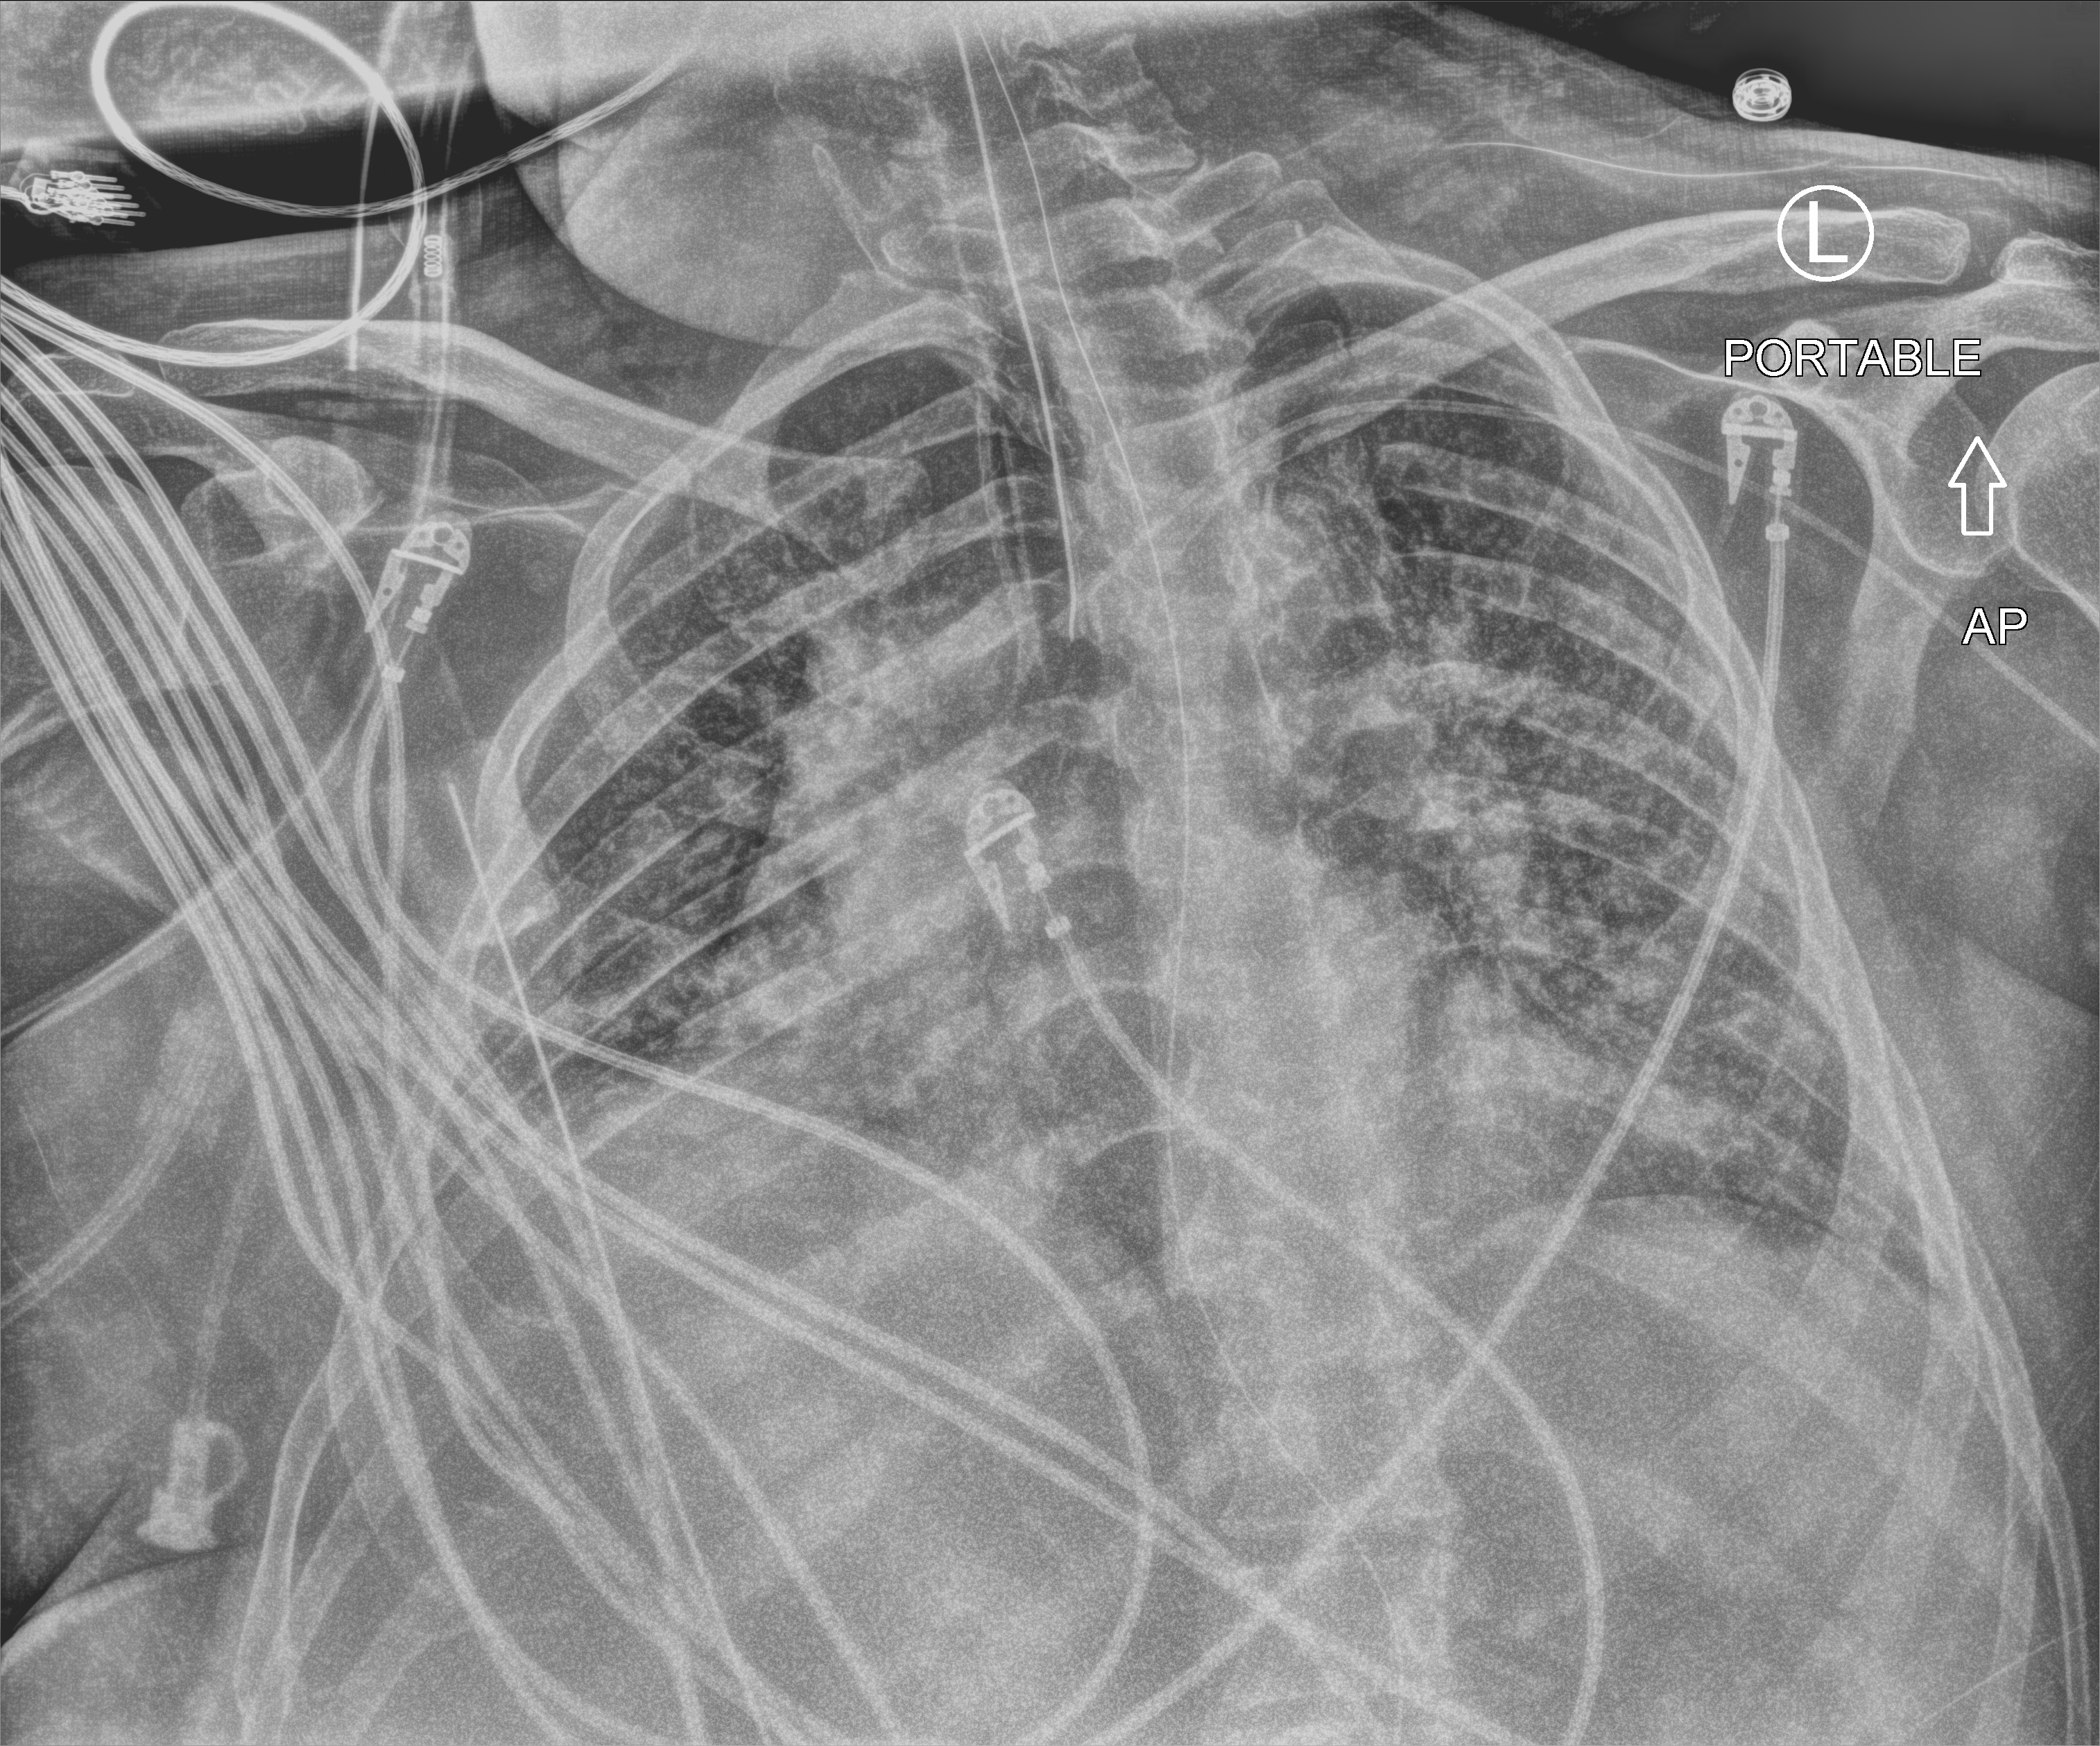
Portable chest radiograph; anteroposterior (AP) projection. Patient hospitalised with COVID-19; male, aged 18–59 years.
Hospital-stay facts (about this admission, not read from this image; timing relative to this image not recorded): diabetes (admission record): no; length of hospital stay: 39 days; mechanically ventilated during this hospital stay: yes.